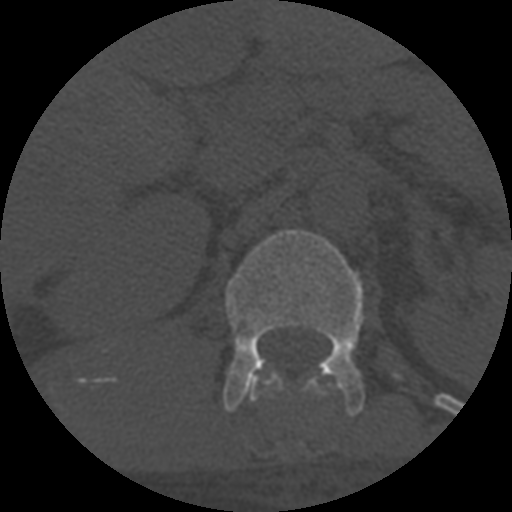
CT including the spine, one axial slice. Slice 295 of 708 in the series (ordered by position). Reconstruction kernel STANDARD. 120 kVp. One of 3 acquisitions stored at this slice position. Bone window (W 1800 / L 400 HU). 1.25 mm slice thickness. 512 × 512 image matrix, field of view 160 × 160 mm. Patient age 55 years. Case-level facts recorded for this patient, not image findings: primary cancer: colon; vertebrae with lytic lesions (as recorded): T12, L1, L5.
Outlined on this slice (semi-automatic segmentation, software-assisted and operator-edited):
- L1 vertebra: bounding box [x1, y1, x2, y2] px = [223, 229, 364, 416]
- T12 vertebra: [248, 373, 323, 402]